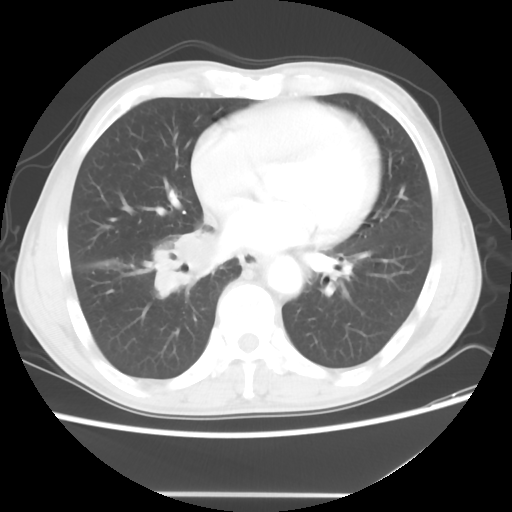
Chest CT, one axial slice. 120 kVp. Lung window (W 1500 / L -600 HU). 5 mm slice thickness. 512 × 512 image matrix. Male patient, age 65 years. Case-level facts recorded for this patient, not image findings: clinical TNM (as recorded): T1c N3 M0; histopathological grade: G3.
Annotated regions visible in this slice (bounding box drawn by a radiologist):
- lung tumour (recorded histology: small cell carcinoma): bounding box <142,223,219,297> (left, top, right, bottom; pixels)